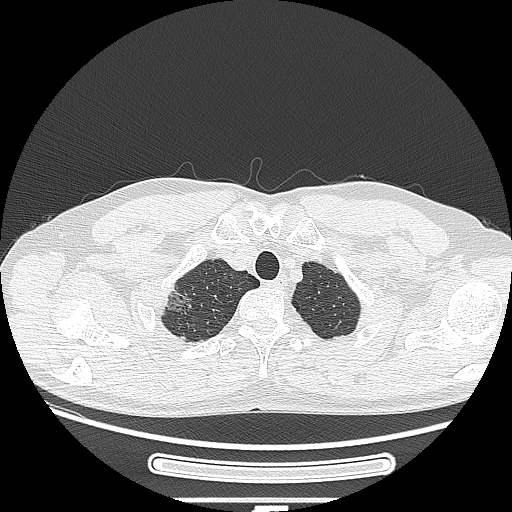
Chest CT, one axial slice; position 238 of 269 along the scan axis; reconstruction kernel LUNG; 120 kVp; lung window (W 1500 / L -600 HU); 512 × 512 image matrix, field of view 382 × 382 mm. Male patient, age 53 years. From the clinical record (not read from this slice): clinical TNM (as recorded): T1c N0 M0; histopathological grade: G2.
Outlined on this slice (bounding box drawn by a radiologist):
- lung tumour (recorded histology: adenocarcinoma): box from (x=157, y=284) to (x=195, y=316) px